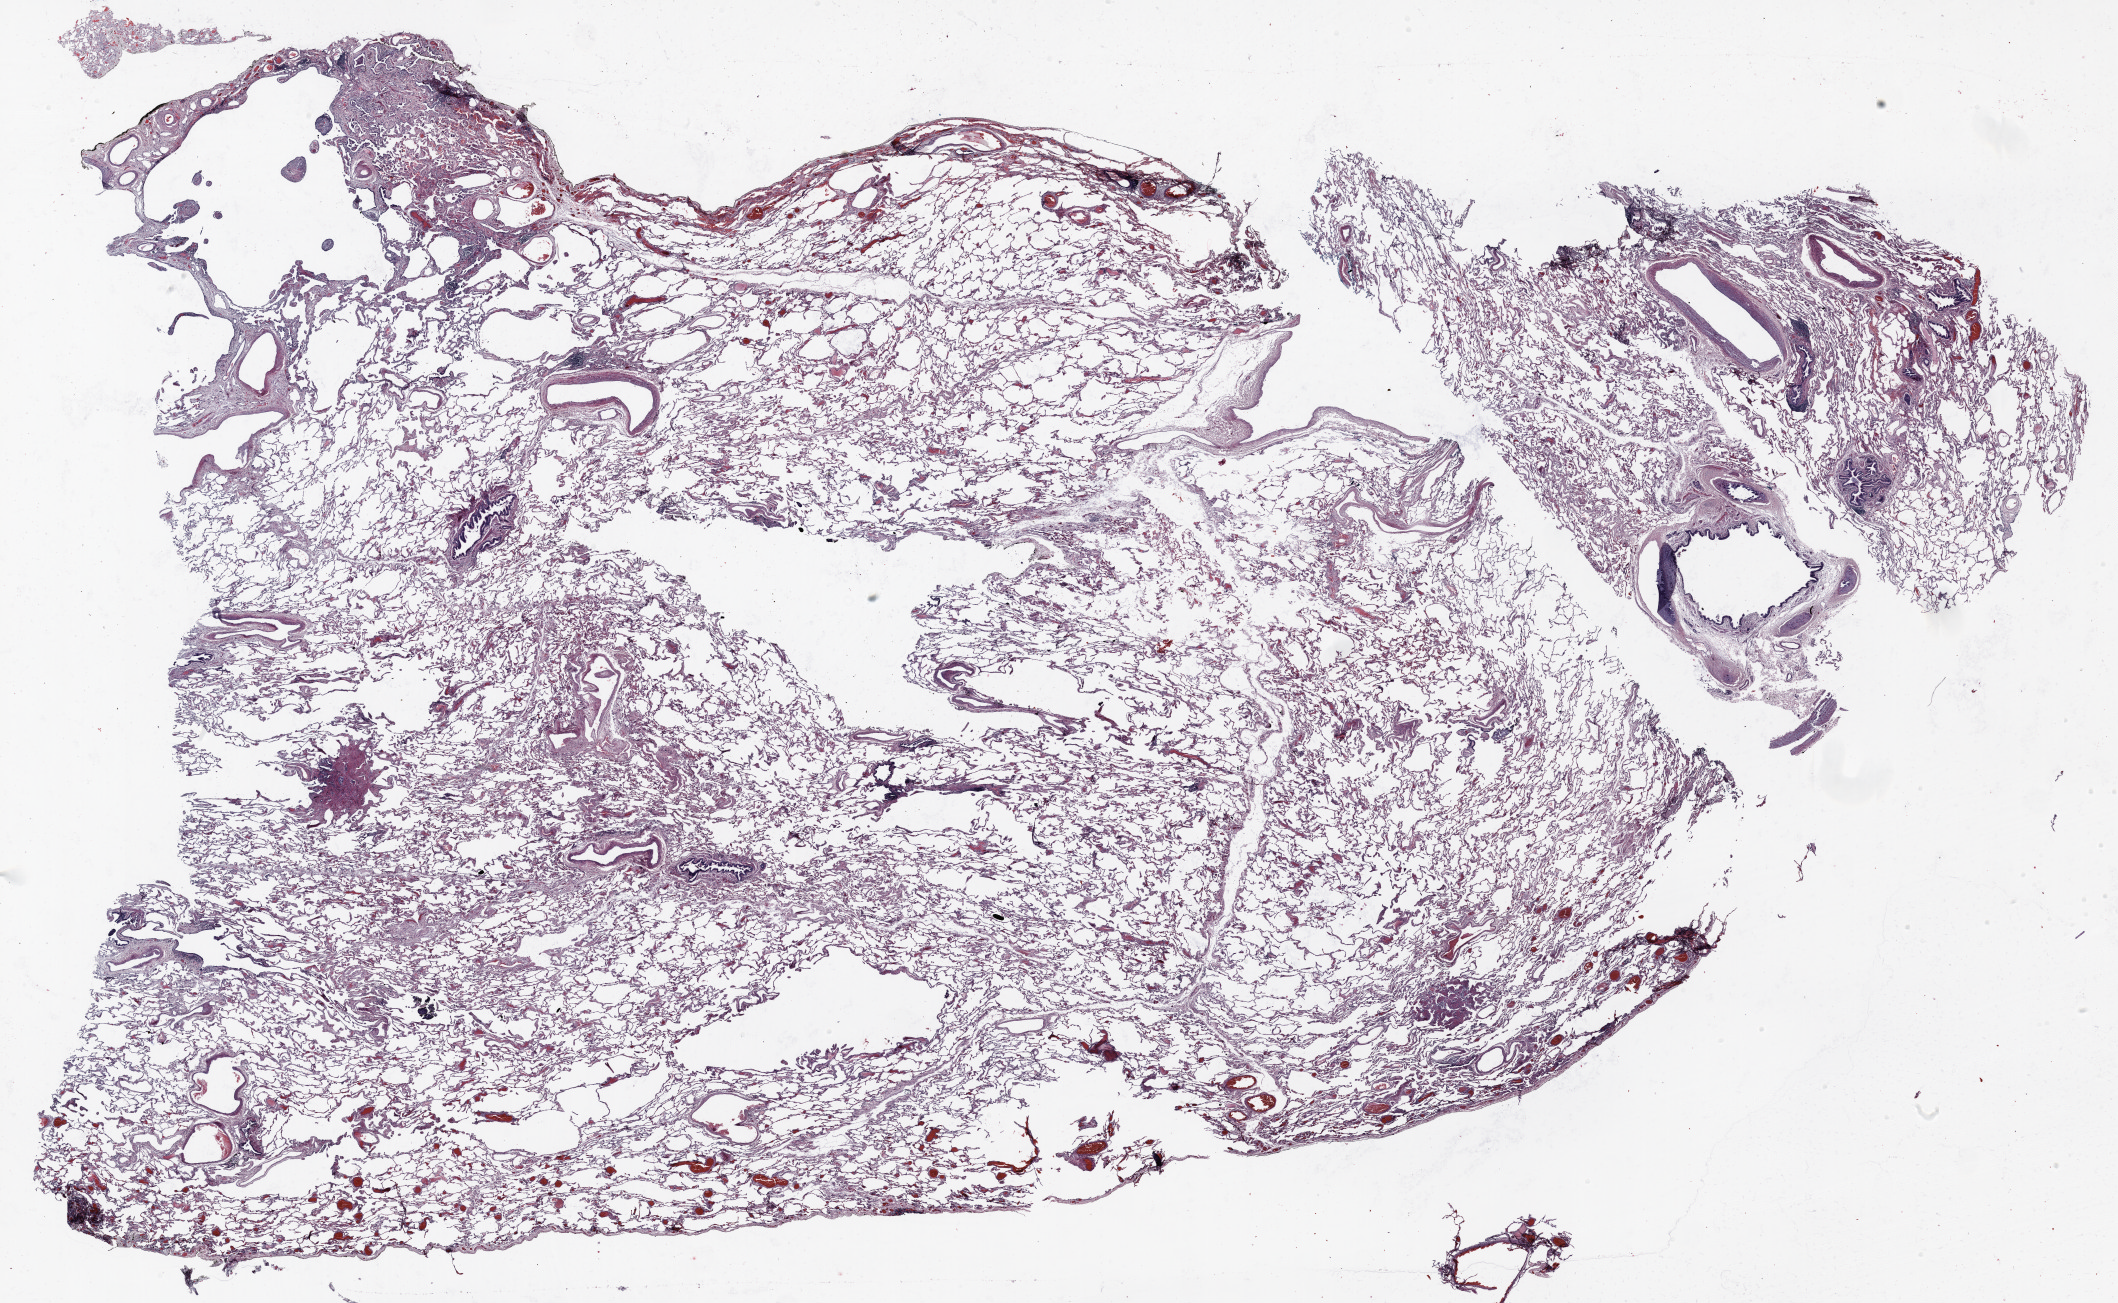
Whole-slide histology image, H&E, shown as a low-resolution overview of the whole scanned area (about 34.0 x 20.9 mm, from a 20x scan), formalin-fixed paraffin-embedded (FFPE) section, lung tissue. Female, age 74 at enrolment. Grade: poorly differentiated (G3).
Participant's lung-cancer diagnosis: Adenocarcinoma, NOS (ICD-O-3 8140/3). Tumour size (pathology): 24 mm. Stage (AJCC 6th edition): IA. Primary tumour location (clinical record): left upper lobe.